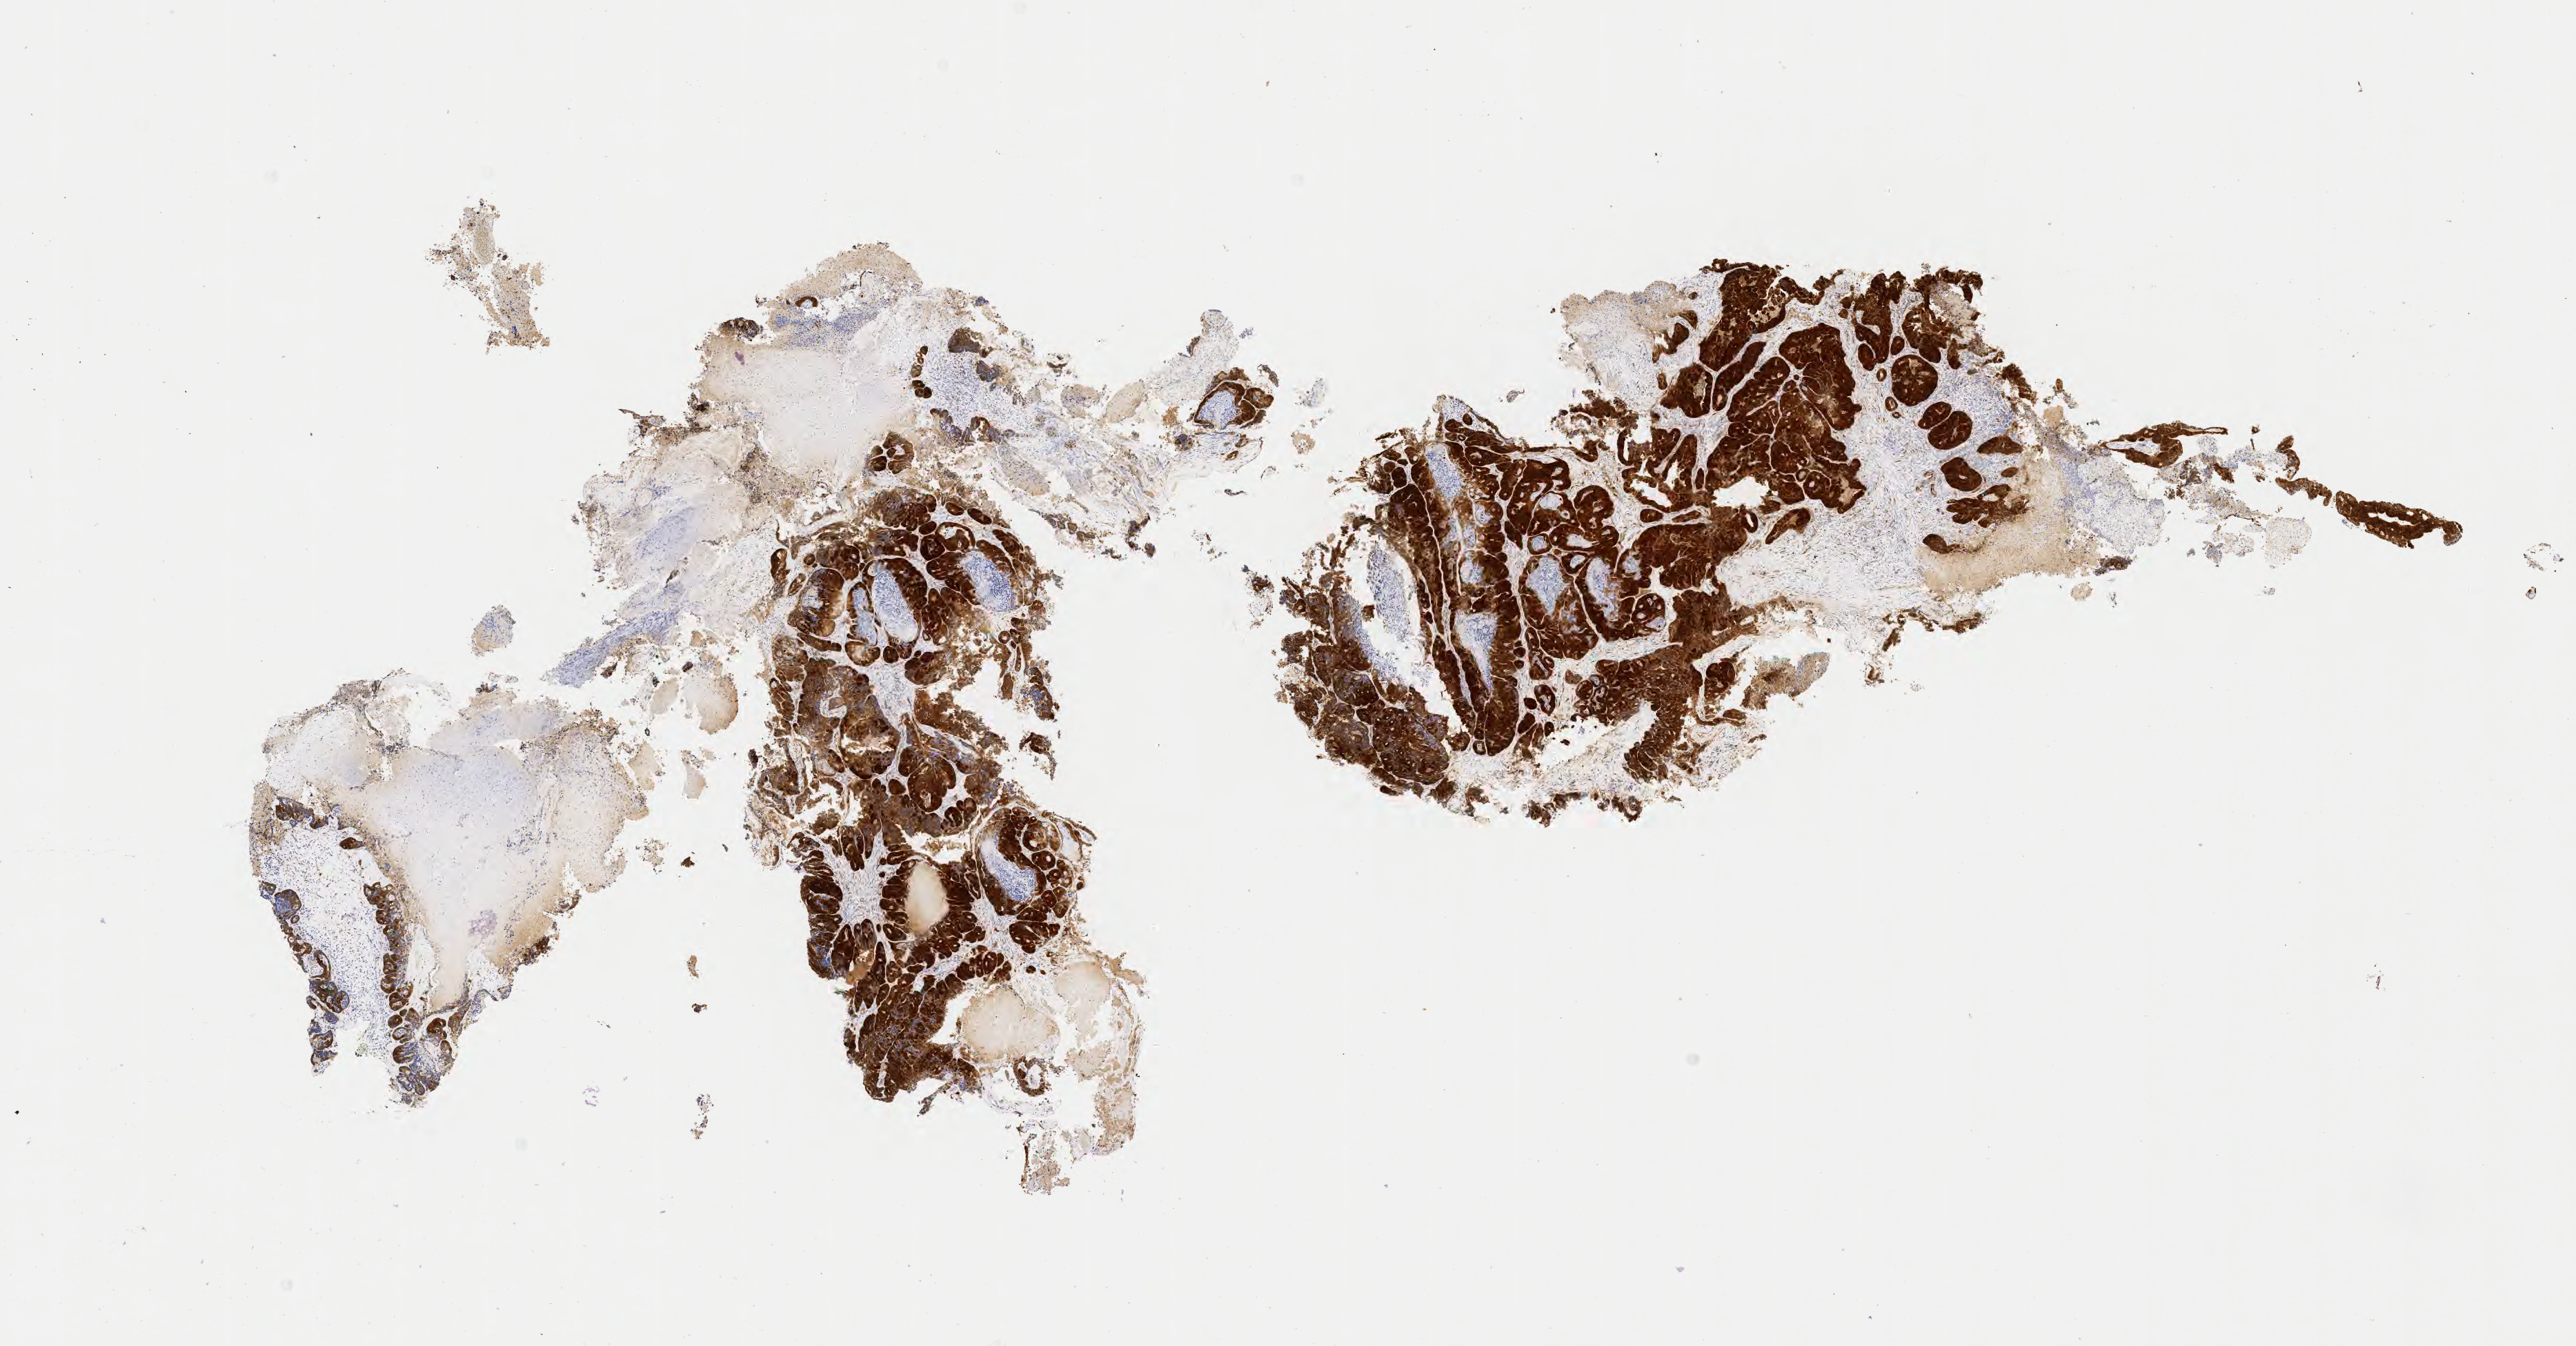
Immunohistochemistry (IHC) whole-slide image stained for p16 (p16INK4a), a low-resolution overview of the entire scanned area, about 15.1 x 7.9 mm, tumor tissue, site: cervix. Patient female; age 48 years.
Histologic diagnosis: Adenocarcinoma, NOS.